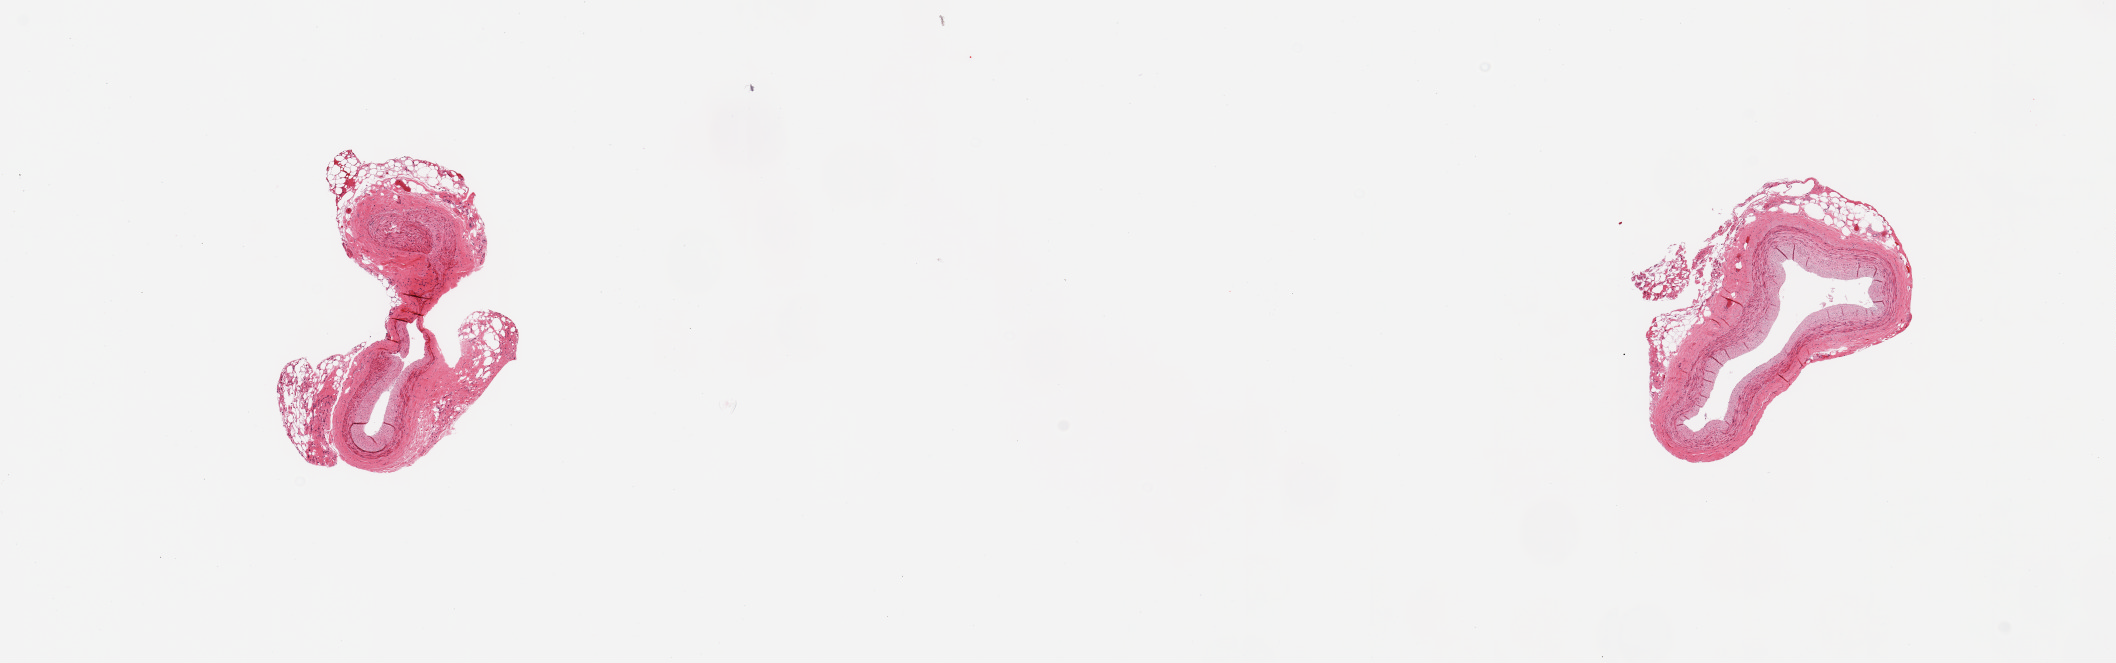
Whole-slide image, H&E stain, brightfield, shown as a low-resolution overview of the whole scanned area (about 16.7 x 5.2 mm, from a 20x scan); PAXgene-fixed, paraffin-embedded tissue; sampled site (target tissue): coronary artery; tissue donor sample. Donor sex: female.
Review note (as recorded): 2 pieces; slight intimal thickening; 30% external fat.